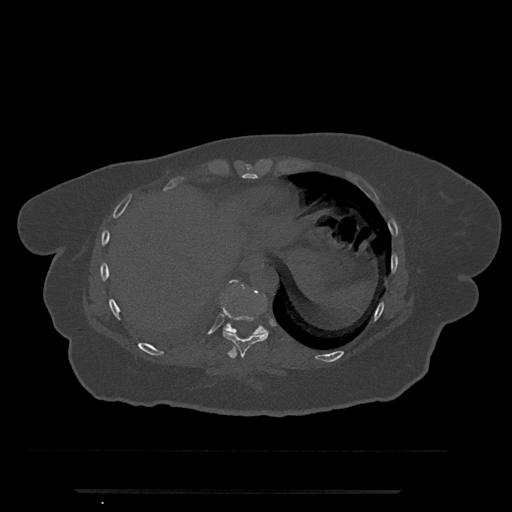
CT including the spine, one axial slice. Position 323 of 797 along the scan axis. Reconstruction kernel Br40s/3. 120 kVp. Bone window (W 1800 / L 400 HU). 0.5 mm slice thickness. 512 × 512 image matrix, field of view 440 × 440 mm. Patient: female, 51 years. Case-level facts recorded for this patient, not image findings: primary cancer: neuro.
Structures marked on this image (semi-automatically segmented with operator editing):
- T10 vertebra: bounding box <223,280,266,336> (left, top, right, bottom; pixels)
- T9 vertebra: <223,304,269,358>